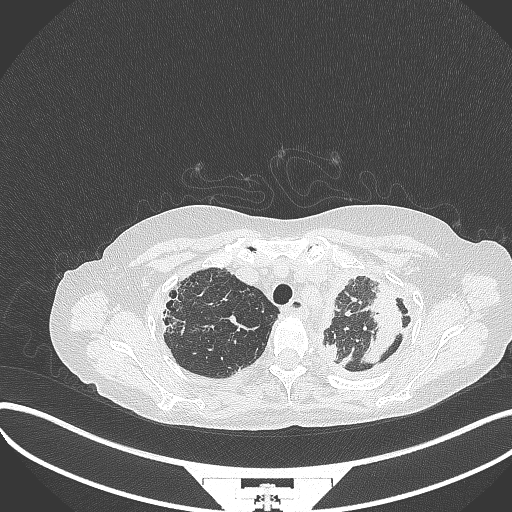
Chest CT, one axial slice. Slice 281 of 373 in the series (ordered by position). Lung window (W 1500 / L -600 HU). 1 mm slice thickness. 512 × 512 image matrix. Patient: female, 56 years. Case-level facts recorded for this patient, not image findings: clinical TNM (as recorded): T1 N0 M0.
Structures marked on this image (bounding box drawn by a radiologist):
- lung tumour (recorded histology: adenocarcinoma): bounding box [x1, y1, x2, y2] px = [358, 288, 409, 367]